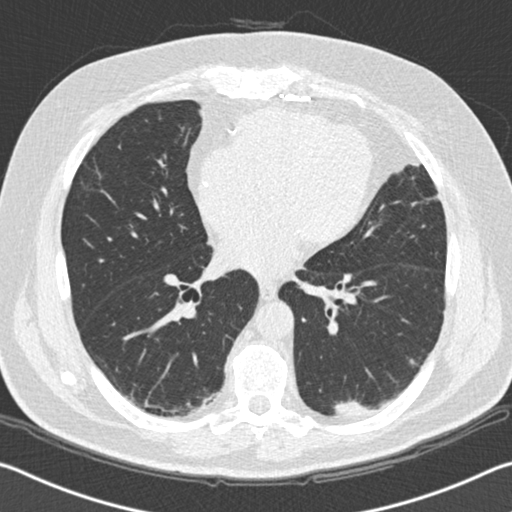
Low-dose screening chest CT, one axial slice. Slice 81 of 172 in the series (ordered by position). Lung window (W 1500 / L -600 HU). 512 × 512 image matrix, field of view 340 × 340 mm.
Outlined on this slice (outlined manually by an expert reader):
- lesion 1 (tumor, lower lobe of left lung): bounding box (x1, y1, x2, y2) in pixels: (333, 399, 375, 417)